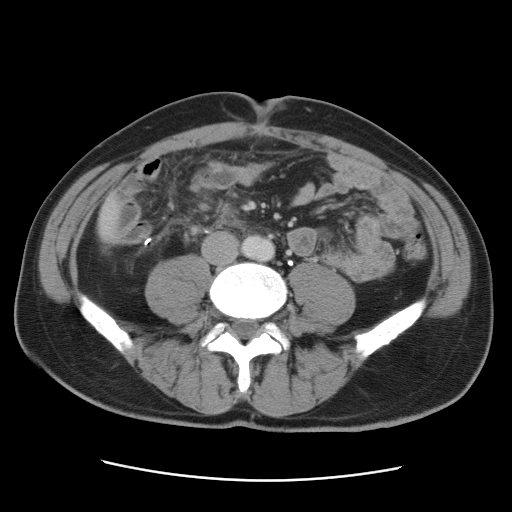
Contrast-enhanced abdominal CT, one axial slice; slice 4 of 89 in the series (ordered by position); soft-tissue window (W 400 / L 40 HU); 5 mm slice thickness; 512 × 512 image matrix, field of view 366 × 366 mm. Male patient, age 59 years. From the clinical record (not read from this slice): diagnosis: colorectal cancer liver metastases, imaged before liver resection; multiple liver metastases: yes; largest metastasis: 0.6 cm; disease in both lobes: yes.
Outlined on this slice (expert manual segmentation):
- liver: box from (x=98, y=201) to (x=120, y=240) px
- planned liver remnant (the part of the liver to remain after resection): (x=99, y=202)–(x=120, y=240)